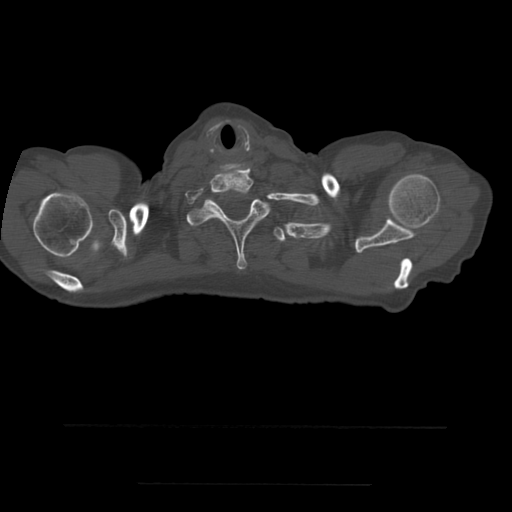
CT including the spine, one axial slice. Position 449 of 544 along the scan axis. Bone window (W 1800 / L 400 HU). 1.25 mm slice thickness. 512 × 512 image matrix, field of view 350 × 350 mm. Patient age 58 years. Case-level facts recorded for this patient, not image findings: primary cancer: lung.
Outlined on this slice (semi-automatically segmented with operator editing):
- T1 vertebra: bounding box <187,194,270,269> (left, top, right, bottom; pixels)
- T2 vertebra: <274,227,286,243>